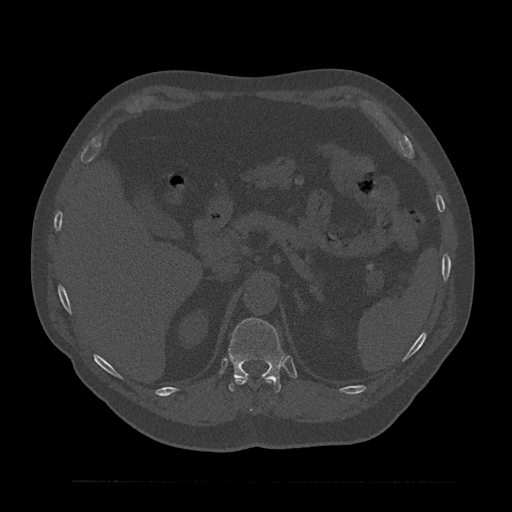
CT including the spine, one axial slice. Position 252 of 797 along the scan axis. 120 kVp. Bone window (W 1800 / L 400 HU). 0.5 mm slice thickness. 512 × 512 image matrix, field of view 430 × 430 mm. Patient: male, 61 years. From the clinical record (not read from this slice): primary cancer: prostate.
Outlined on this slice (semi-automatically segmented with operator editing):
- T11 vertebra: bounding box (x1, y1, x2, y2) in pixels: (235, 378, 273, 412)
- T12 vertebra: (228, 318, 285, 393)